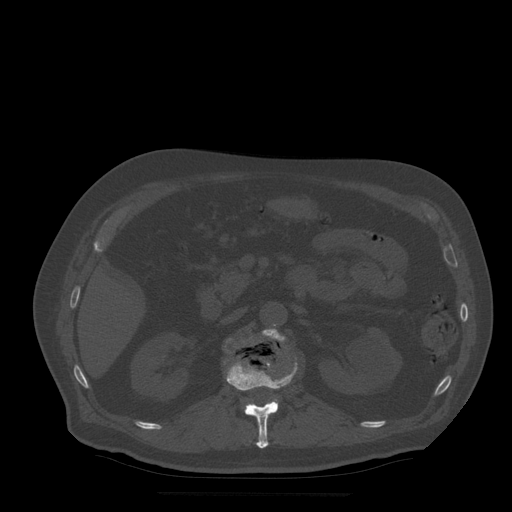
CT including the spine, one axial slice; slice 188 of 522 in the series (ordered by position); bone window (W 1800 / L 400 HU); 1.25 mm slice thickness; 512 × 512 image matrix, field of view 420 × 420 mm. Patient age 72 years. Case-level facts recorded for this patient, not image findings: primary cancer: prostate.
Outlined on this slice (semi-automatic segmentation, software-assisted and operator-edited):
- L1 vertebra: bounding box [x1, y1, x2, y2] px = [227, 339, 298, 449]
- L2 vertebra: [263, 329, 285, 414]